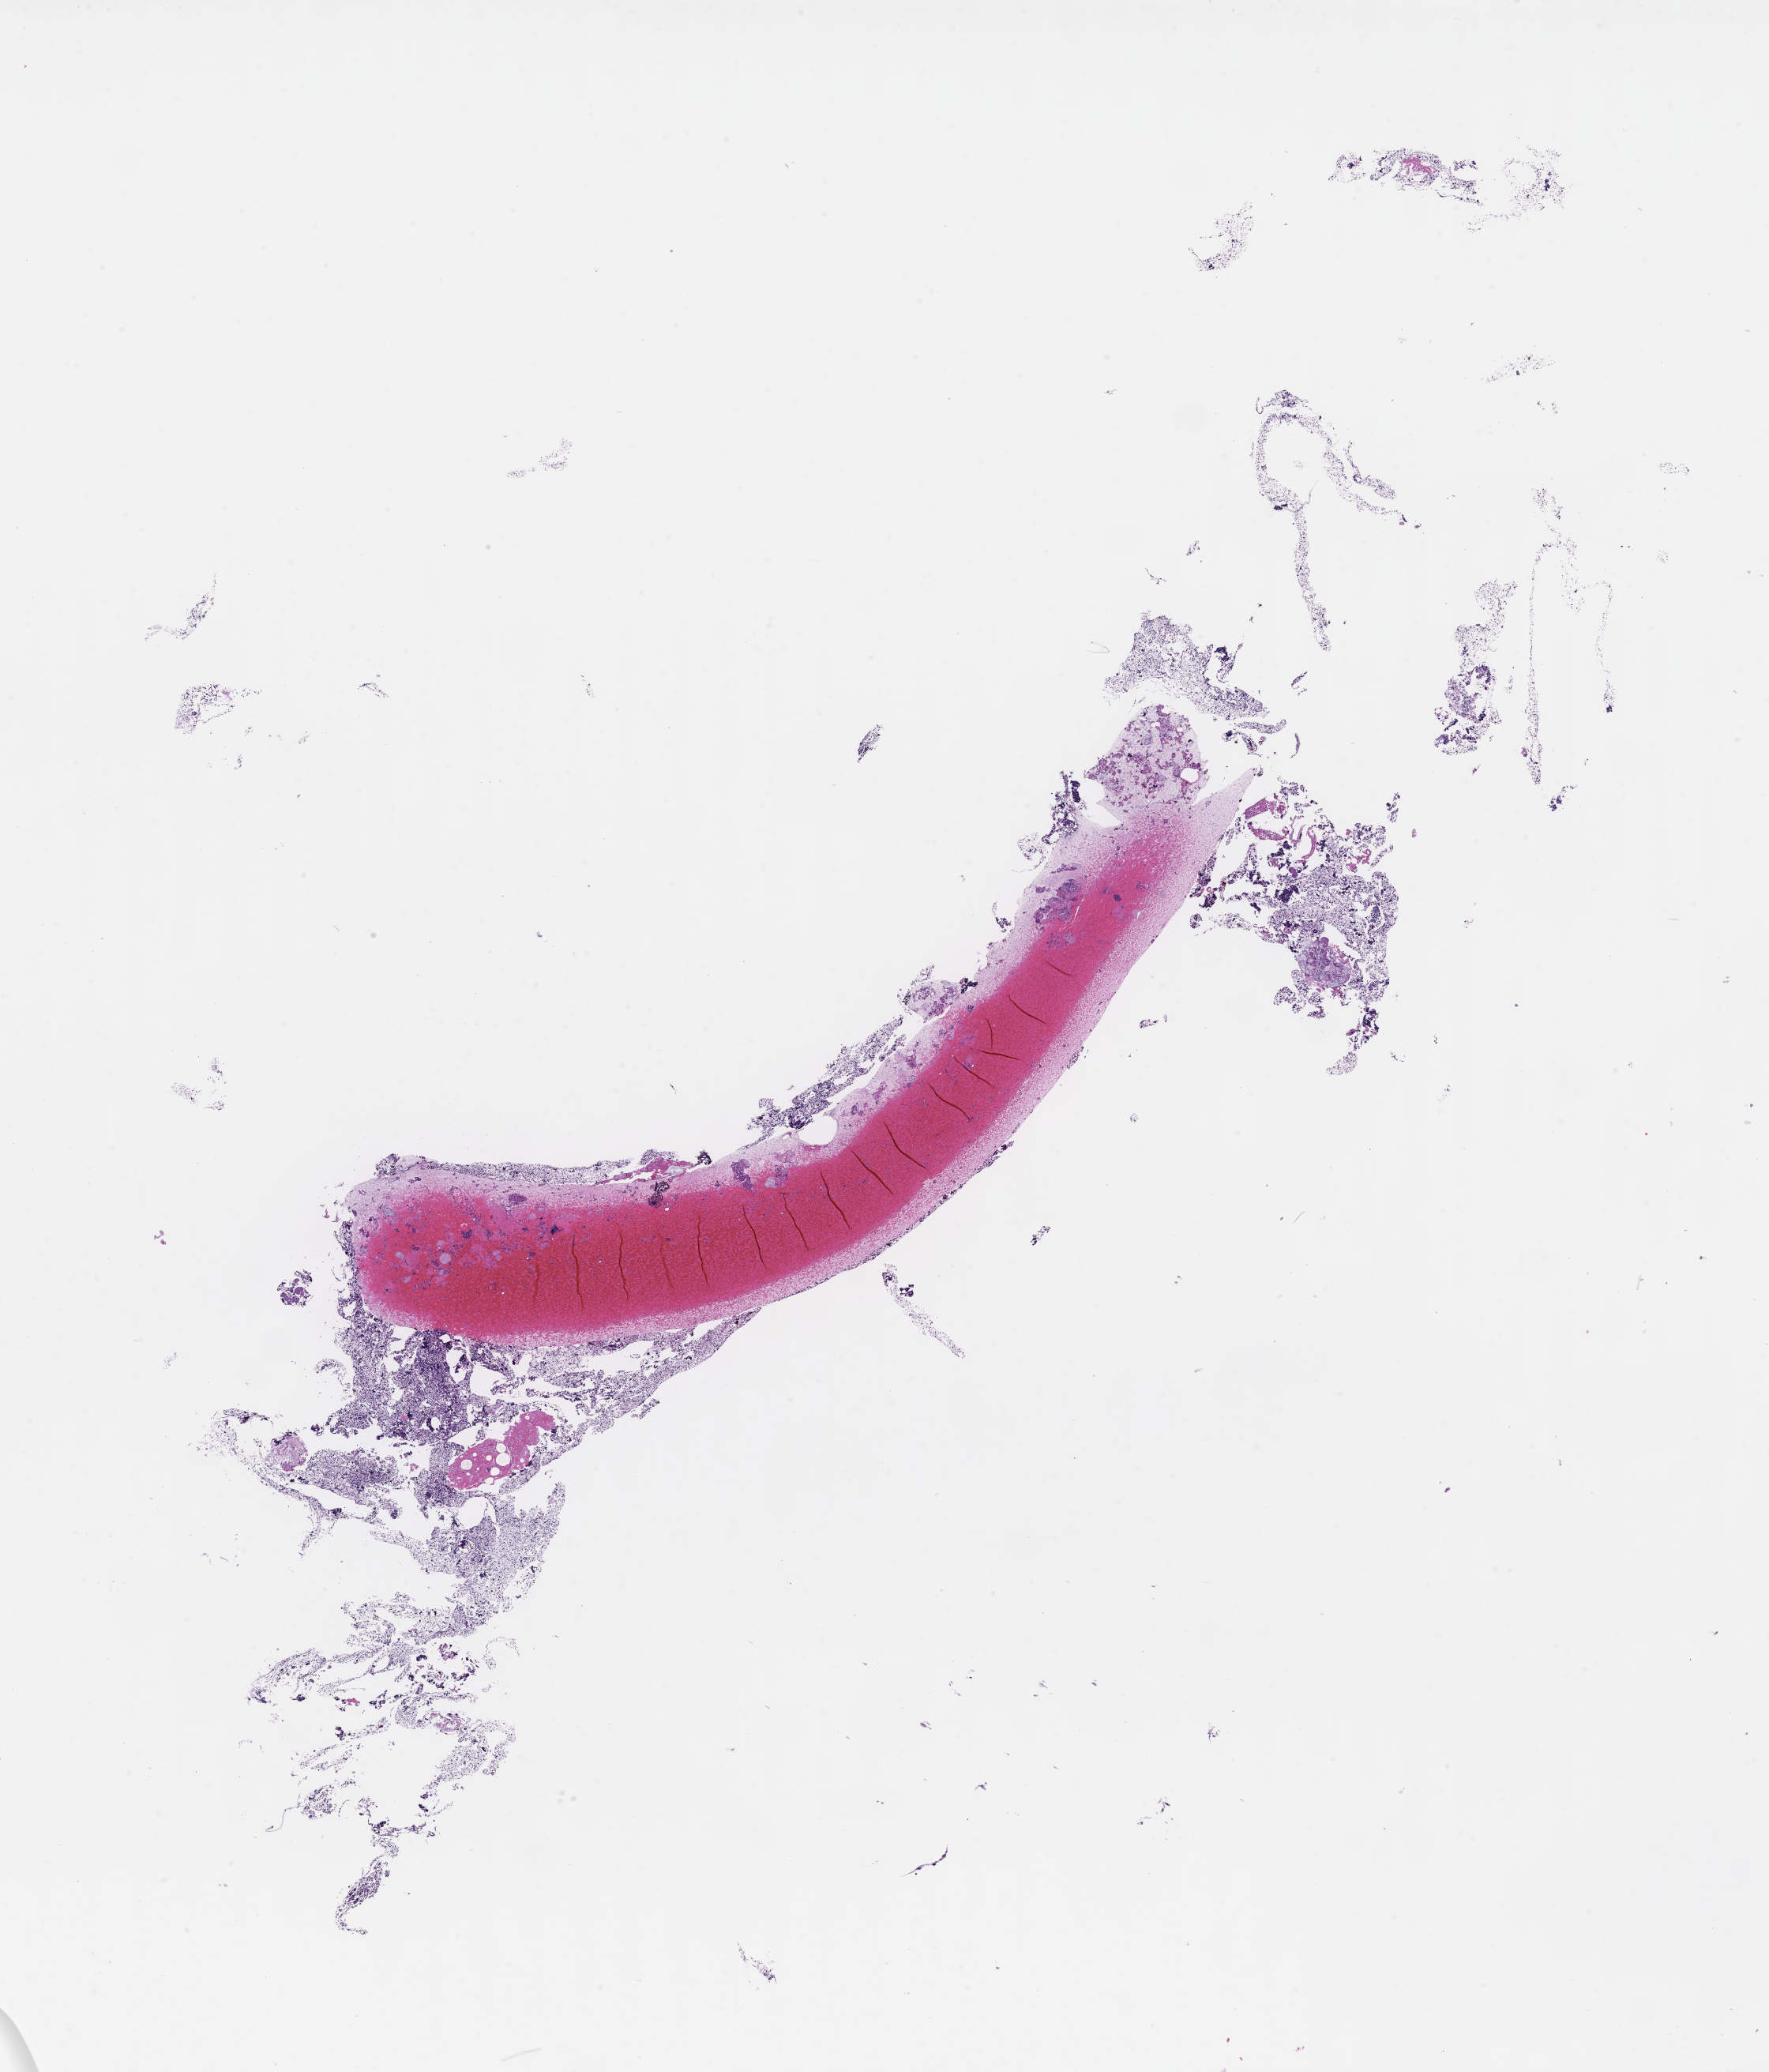
Digitized hematoxylin and eosin (H&E)-stained section — low-resolution overview of the scanned area, about 18.1 x 21.2 mm, formalin-fixed, paraffin-embedded (FFPE) tissue, tissue site: bone marrow, specimen time point: archival tissue. Male patient.
• this section: primary tumor
• diagnosis: Plasma Cell Myeloma